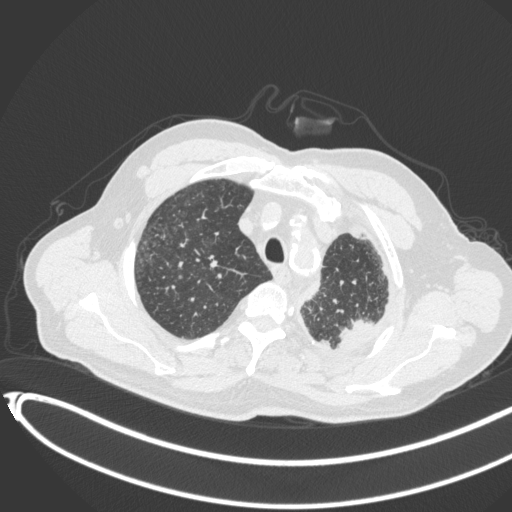
Chest CT, one axial slice. Slice 356 of 451 in the series (ordered by position). Reconstruction kernel B31f. 120 kVp. Lung window (W 1500 / L -600 HU). 1 mm slice thickness. 512 × 512 image matrix, field of view 400 × 400 mm. Patient: male, 78 years. From the clinical record (not read from this slice): clinical TNM (as recorded): T1c N0 M1.
Outlined on this slice (bounding box drawn by a radiologist):
- lung tumour (recorded histology: adenocarcinoma): box from (x=337, y=314) to (x=381, y=354) px